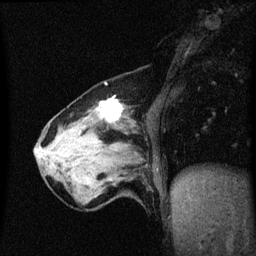
Breast MRI (dynamic contrast-enhanced), one sagittal slice. Dynamic contrast-enhanced series, image 2 of 3 at this slice position (ordered by acquisition). 1.5 T. TE 4.2 ms, TR 8.4 ms. 2 mm slice thickness. 256 × 256 image matrix, field of view 200 × 200 mm. Female patient, age 64 years. Case-level facts recorded for this patient, not image findings: setting: breast cancer imaged before/during neoadjuvant chemotherapy; receptor status: HR-positive, HER2-negative.
Structures marked on this image (semi-automatic segmentation, software-assisted and operator-edited):
- analysis volume of interest (the breast-tissue region the enhancement analysis was run in; not a lesion): bounding box <56,96,142,175> (left, top, right, bottom; pixels)
- tumour enhancement mask (voxels above the 70 % enhancement threshold inside the analysis volume of interest): <101,100,124,121>